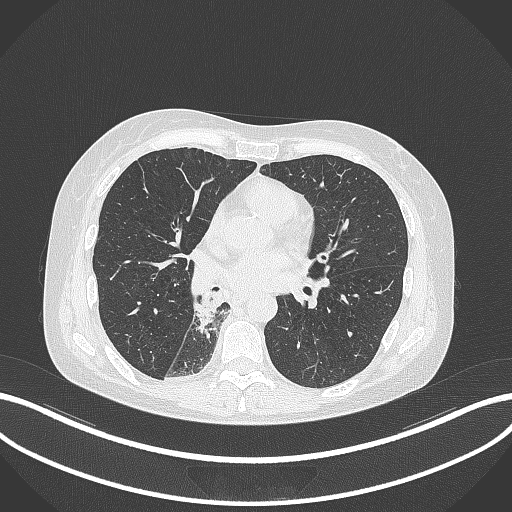
Chest CT, one axial slice. Slice 148 of 329 in the series (ordered by position). Reconstruction kernel B70f. 120 kVp. Lung window (W 1500 / L -600 HU). 512 × 512 image matrix, field of view 400 × 400 mm. Patient: female, 63 years. From the clinical record (not read from this slice): clinical TNM (as recorded): T1c N0 M0.
Structures marked on this image (bounding box drawn by a radiologist):
- lung tumour (recorded histology: adenocarcinoma): bounding box [x1, y1, x2, y2] px = [197, 290, 221, 334]